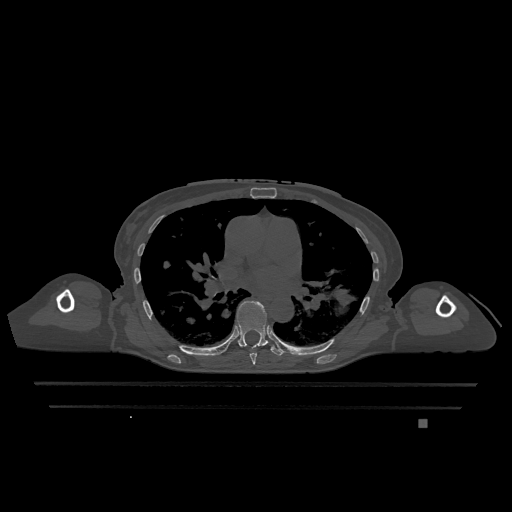
CT including the spine, one axial slice; slice 758 of 1317 in the series (ordered by position); bone window (W 1800 / L 400 HU); 0.5 mm slice thickness; 512 × 512 image matrix. Female patient, age 74 years. From the clinical record (not read from this slice): primary cancer: lung; vertebrae with lytic lesions (as recorded): T1, T4, T5, T6, L4, L5.
Structures marked on this image (semi-automatic segmentation, software-assisted and operator-edited):
- T6 vertebra: bounding box (x1, y1, x2, y2) in pixels: (242, 346, 257, 365)
- T7 vertebra: (223, 300, 283, 356)